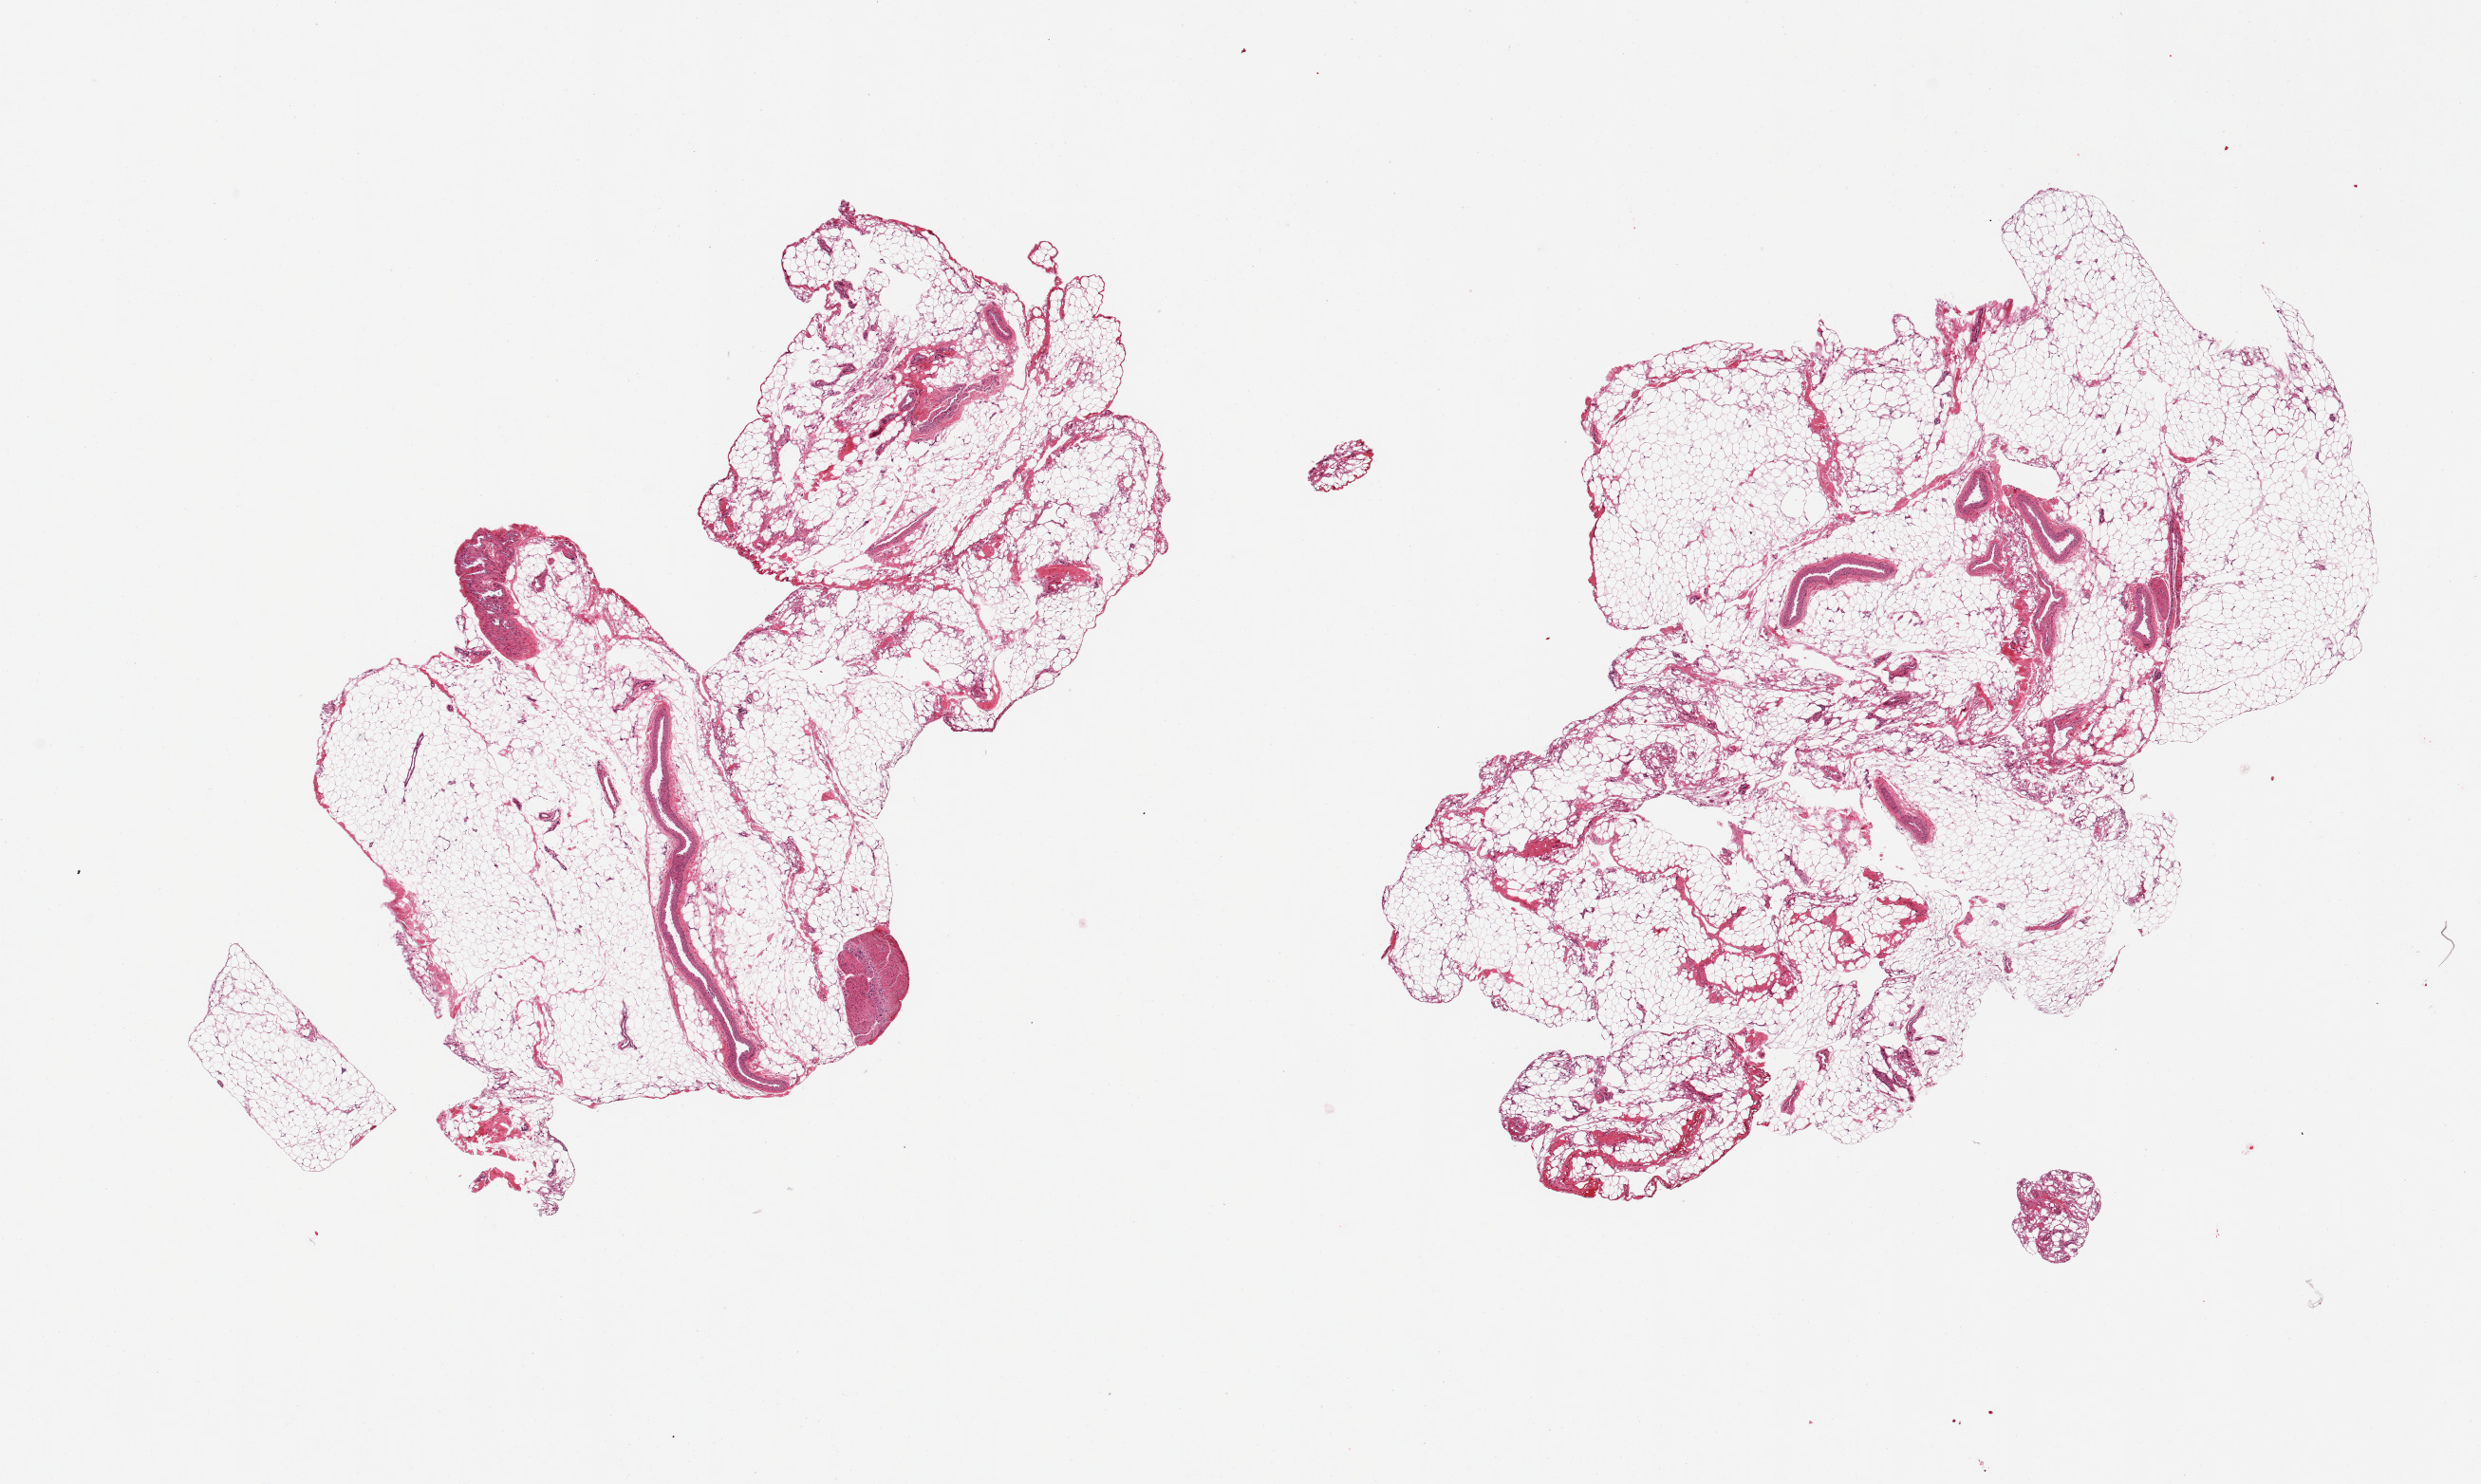
Whole-slide image, H&E stain, low-resolution overview of the scanned area, about 20.7 x 12.4 mm. PAXgene-fixed, paraffin-embedded tissue. Target tissue: omentum. Tissue donor sample. Donor: female.
* pathologist's review note for this sample: 2 pieces, ~10% fascia/vascular elements